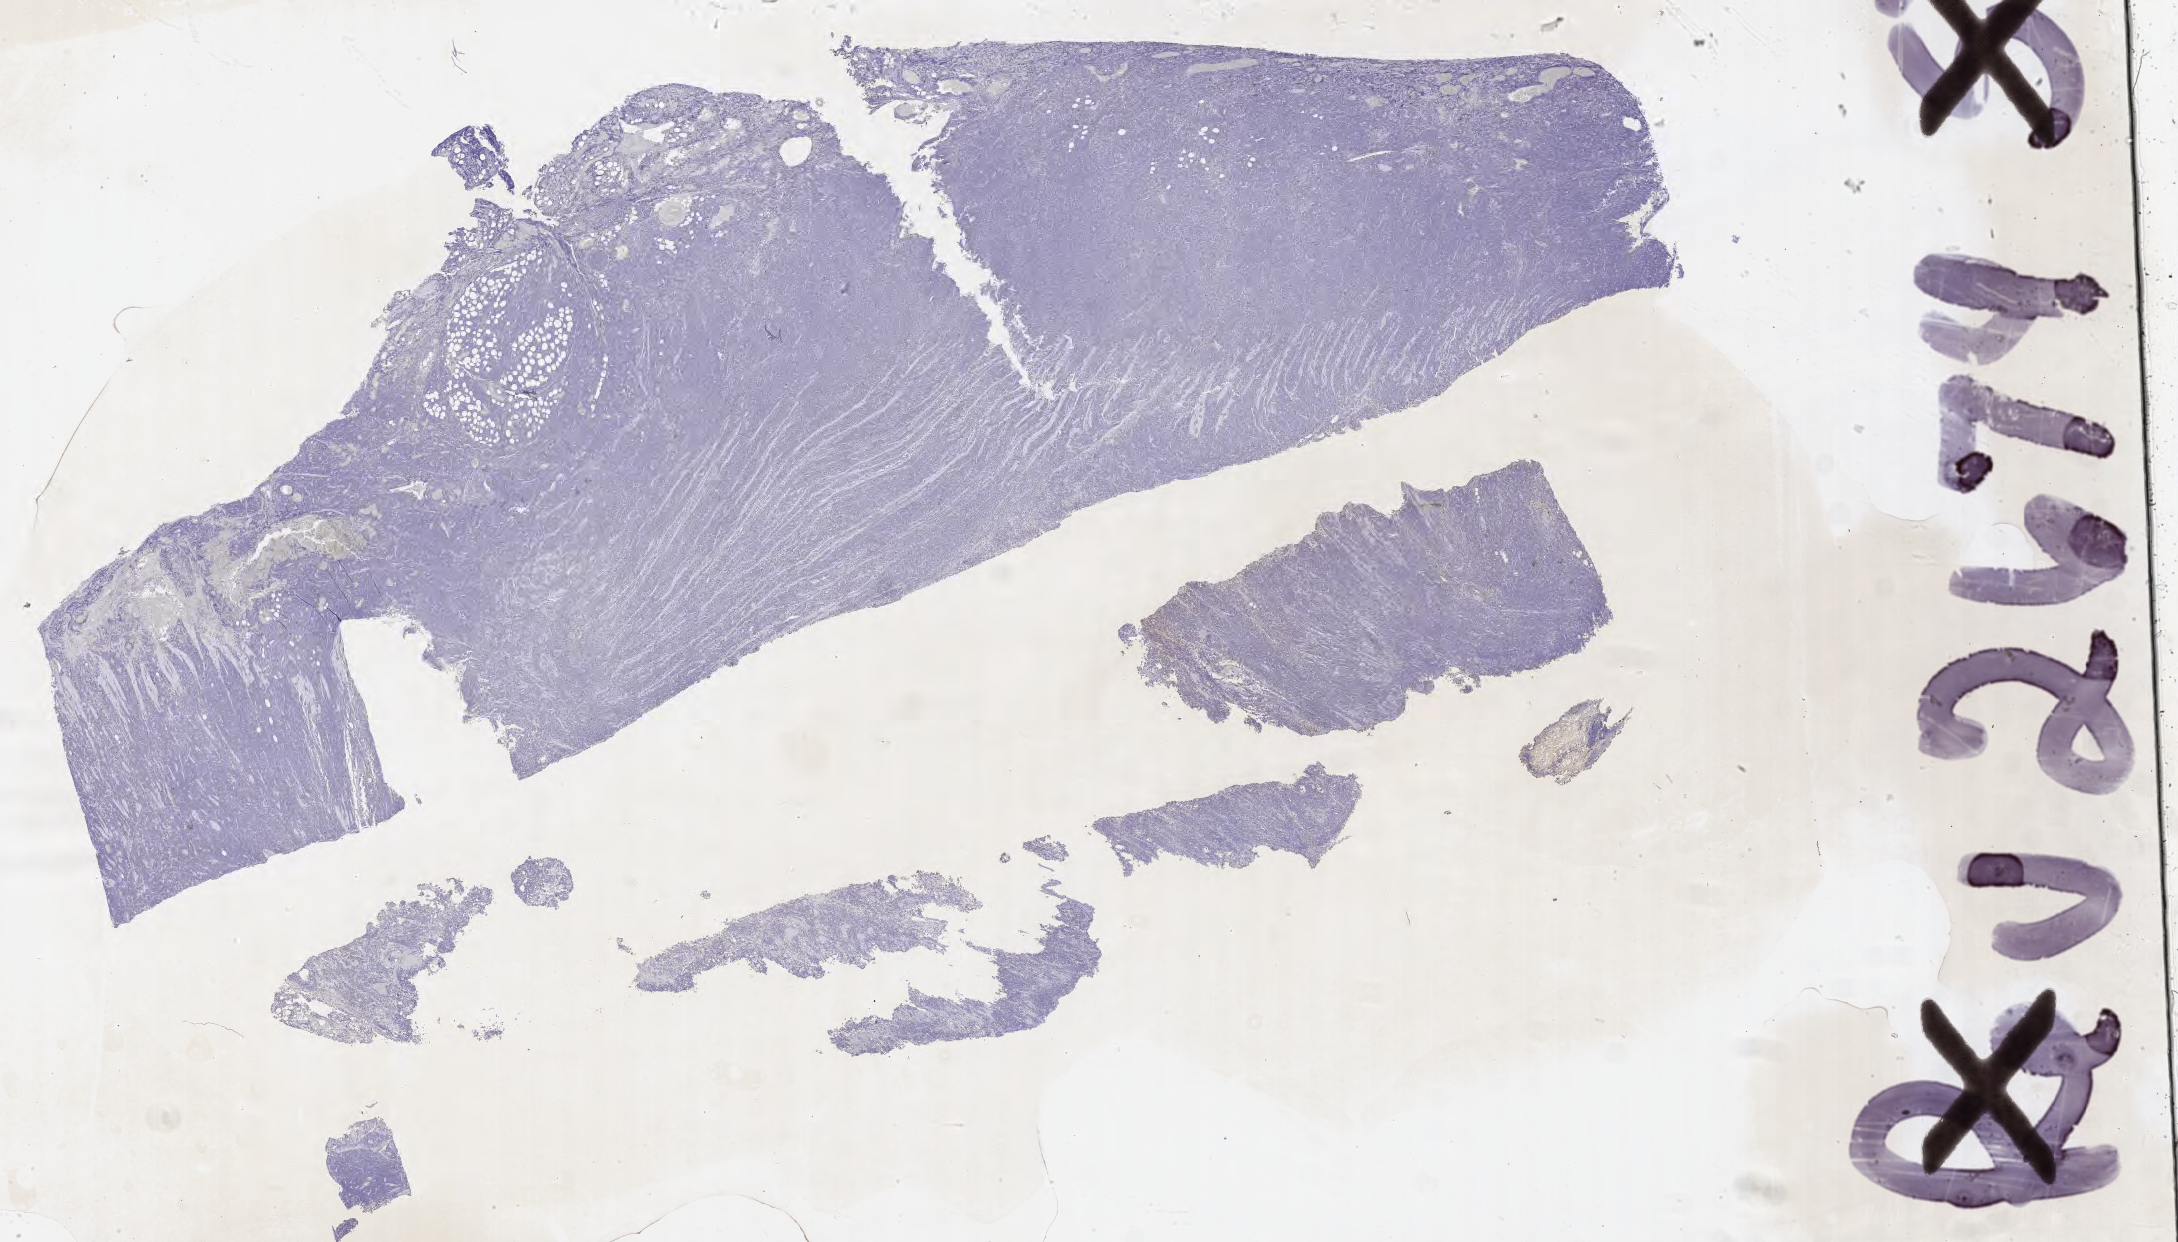
Immunohistochemistry (IHC) whole-slide image stained for CD5 — shown as a low-resolution overview of the whole scanned area (about 35.2 x 20.1 mm), tumor tissue. Patient male; aged 56.
Diagnosis: Burkitt lymphoma, NOS.